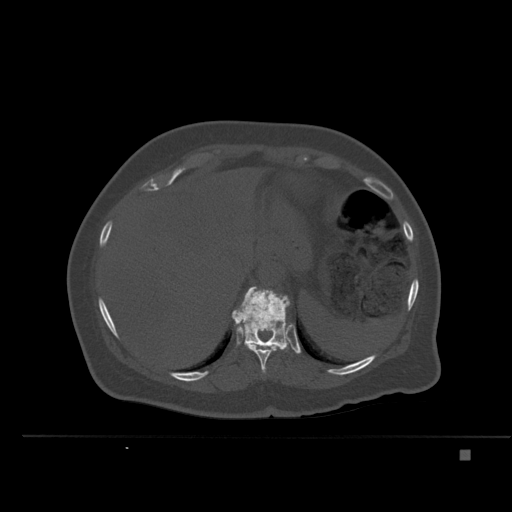
CT including the spine, one axial slice; position 274 of 477 along the scan axis; bone window (W 1800 / L 400 HU); 1.5 mm slice thickness; 512 × 512 image matrix. Patient: female, 74 years. Case-level facts recorded for this patient, not image findings: primary cancer: colon.
Outlined on this slice (semi-automatic segmentation, software-assisted and operator-edited):
- T10 vertebra: bounding box <245,342,280,374> (left, top, right, bottom; pixels)
- T11 vertebra: <232,286,290,350>